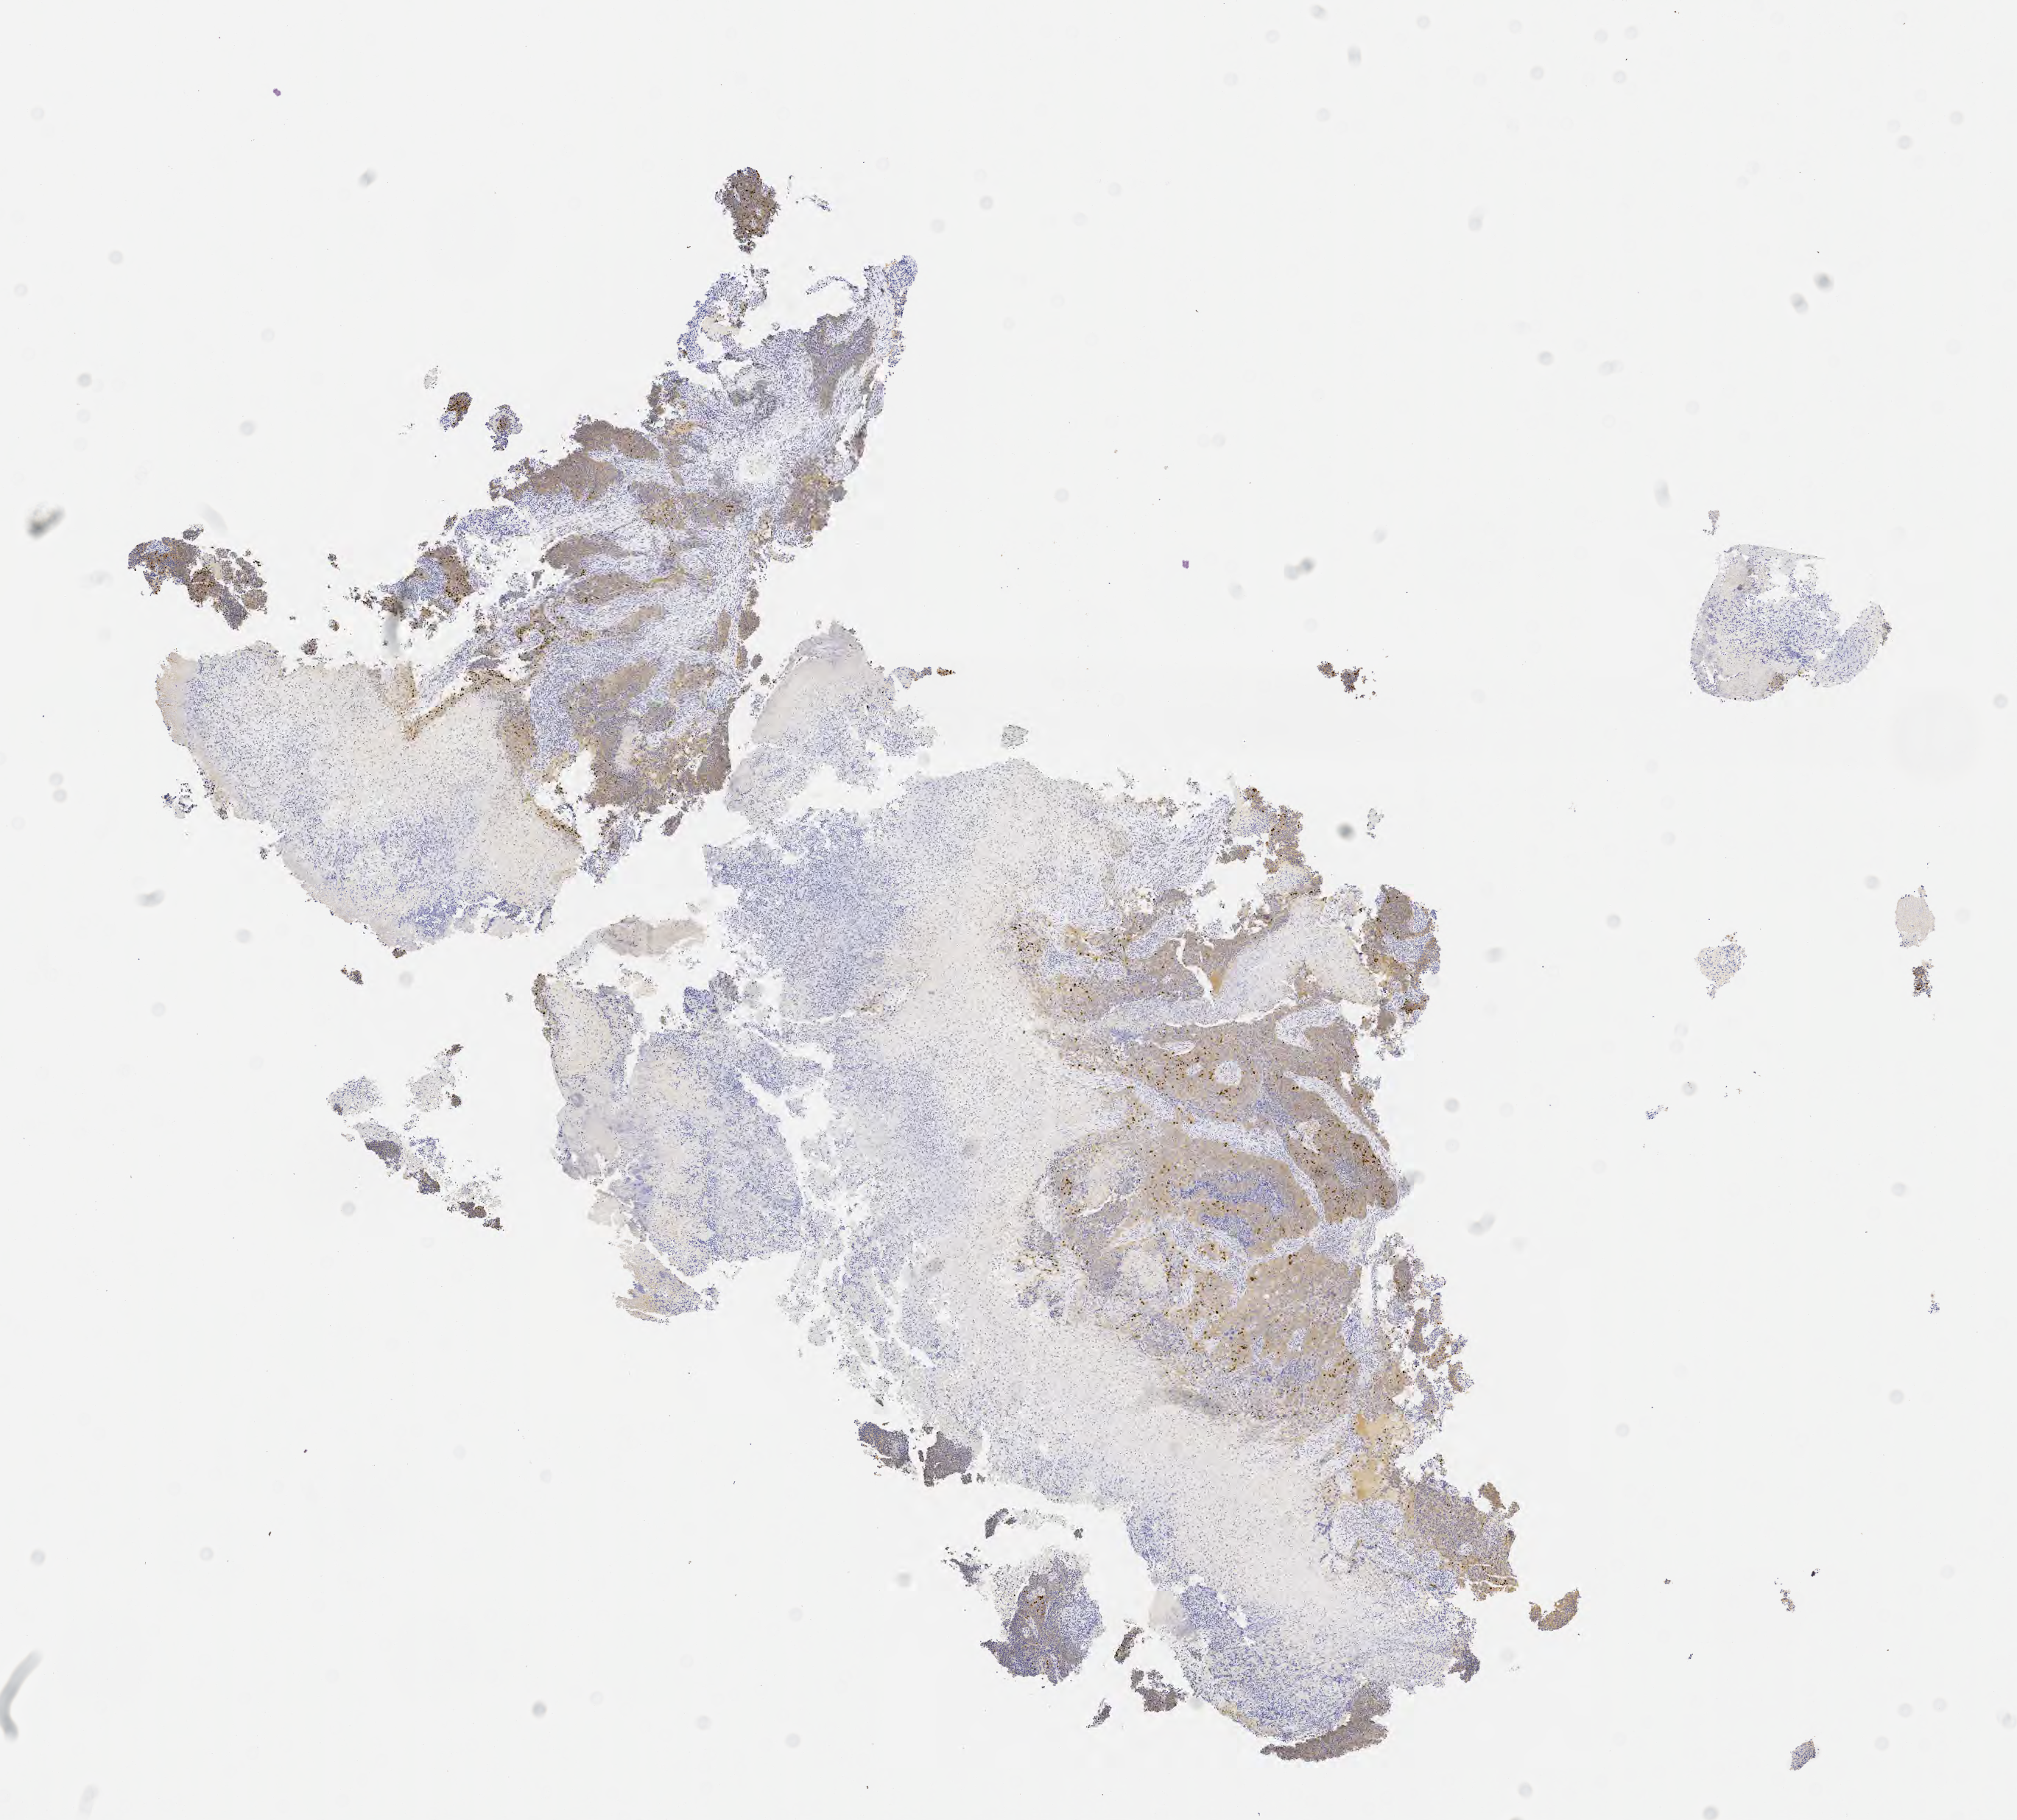
Immunohistochemistry (IHC) whole-slide image stained for p63, shown as a low-resolution overview of the whole scanned area (about 11.1 x 10.0 mm); tumor tissue; site: cervix. Patient female; age 65 years.
Histologic diagnosis: Squamous cell carcinoma, large cell, nonkeratinizing, NOS.